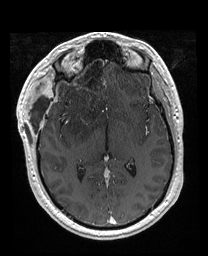
Brain MRI from a brain-tumour surgery series, one axial slice; position 99 of 176 along the scan axis; T1-weighted post-contrast; 1 mm slice thickness; 208 × 256 image matrix, field of view 208 × 256 mm. Case-level facts recorded for this patient, not image findings: histopathology: Astrocytoma; WHO grade: 4.
Annotated regions visible in this slice (manually delineated by an expert):
- previous resection cavity: bounding box [x1, y1, x2, y2] px = [56, 53, 106, 84]